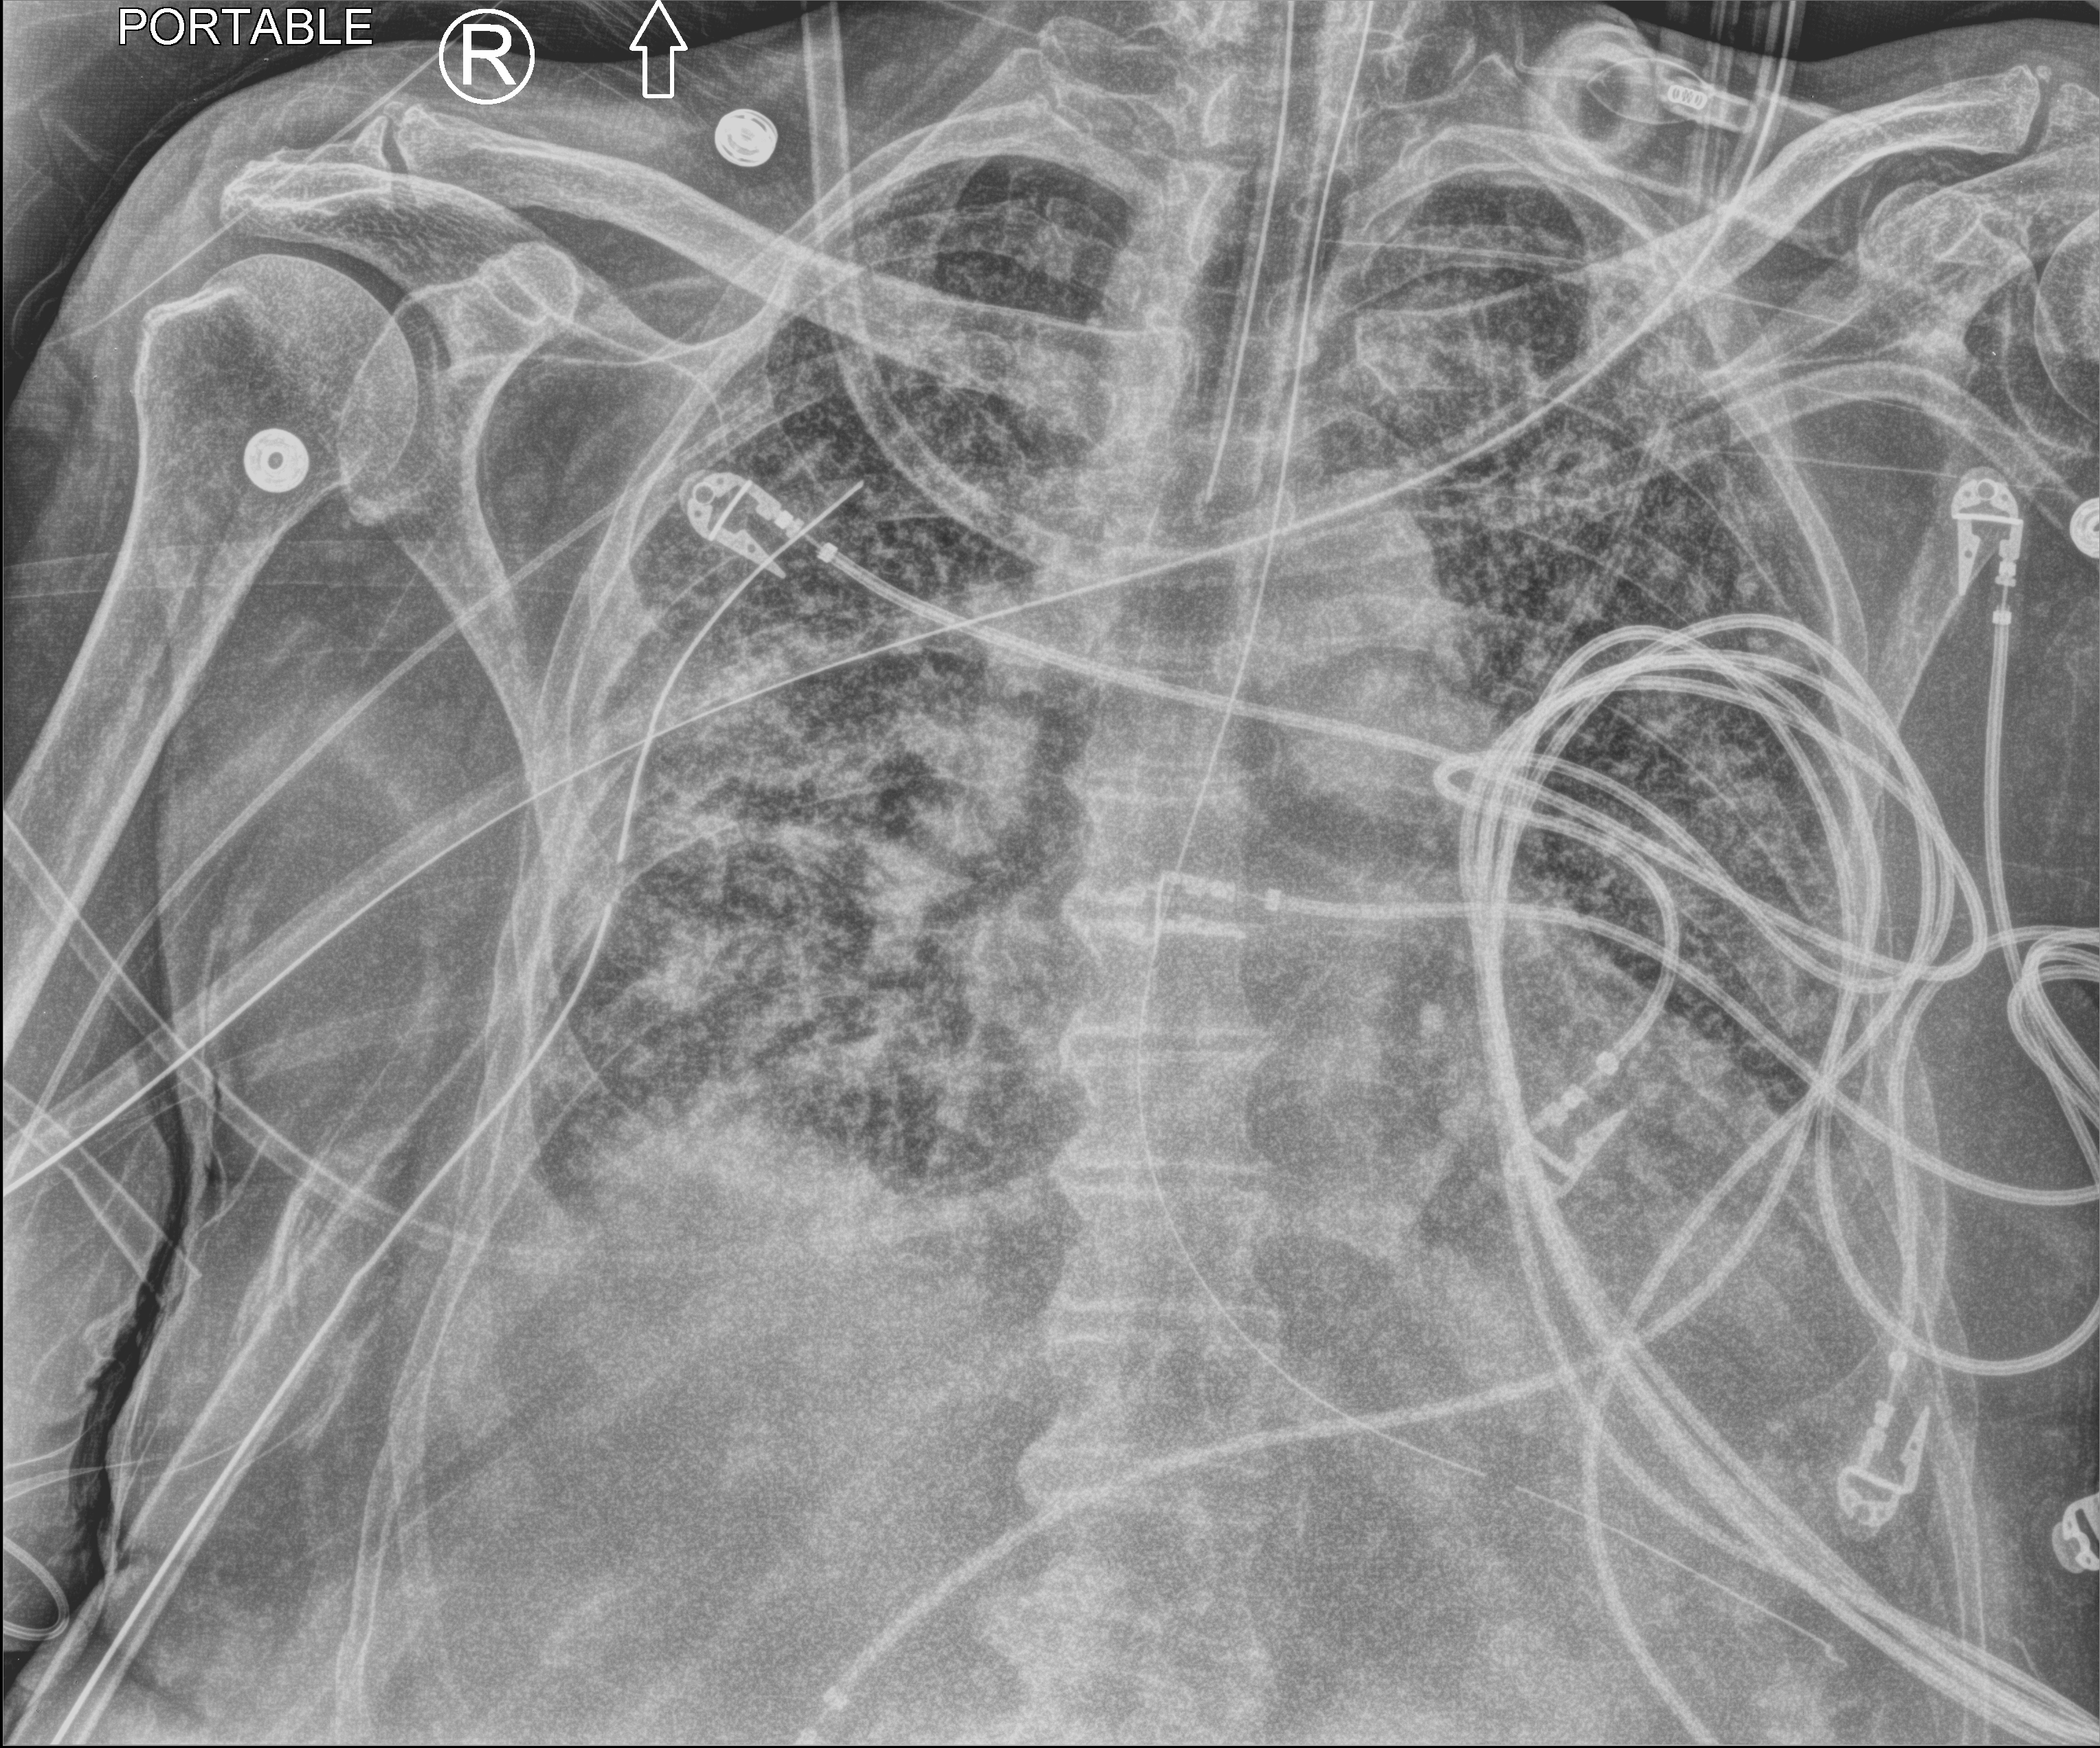
Portable chest radiograph; anteroposterior (AP) projection. Male patient hospitalised with COVID-19, age 75–90 years.
Hospital-stay facts (about this admission, not read from this image; timing relative to this image not recorded): mechanically ventilated during this hospital stay: yes.